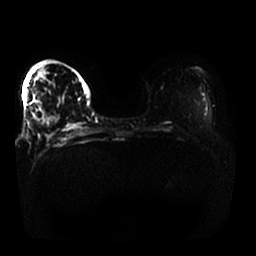
Breast MRI, one axial slice; position 12 of 25 along the scan axis; diffusion-weighted series; image 2 of 4 stored at this slice position (different b-values; order by instance number); 1.5 T; 4 mm slice thickness; 256 × 256 image matrix, field of view 370 × 370 mm. Female patient.
Structures marked on this image (manually delineated by an expert):
- tumour on diffusion-weighted imaging: bounding box <40,119,46,126> (left, top, right, bottom; pixels)